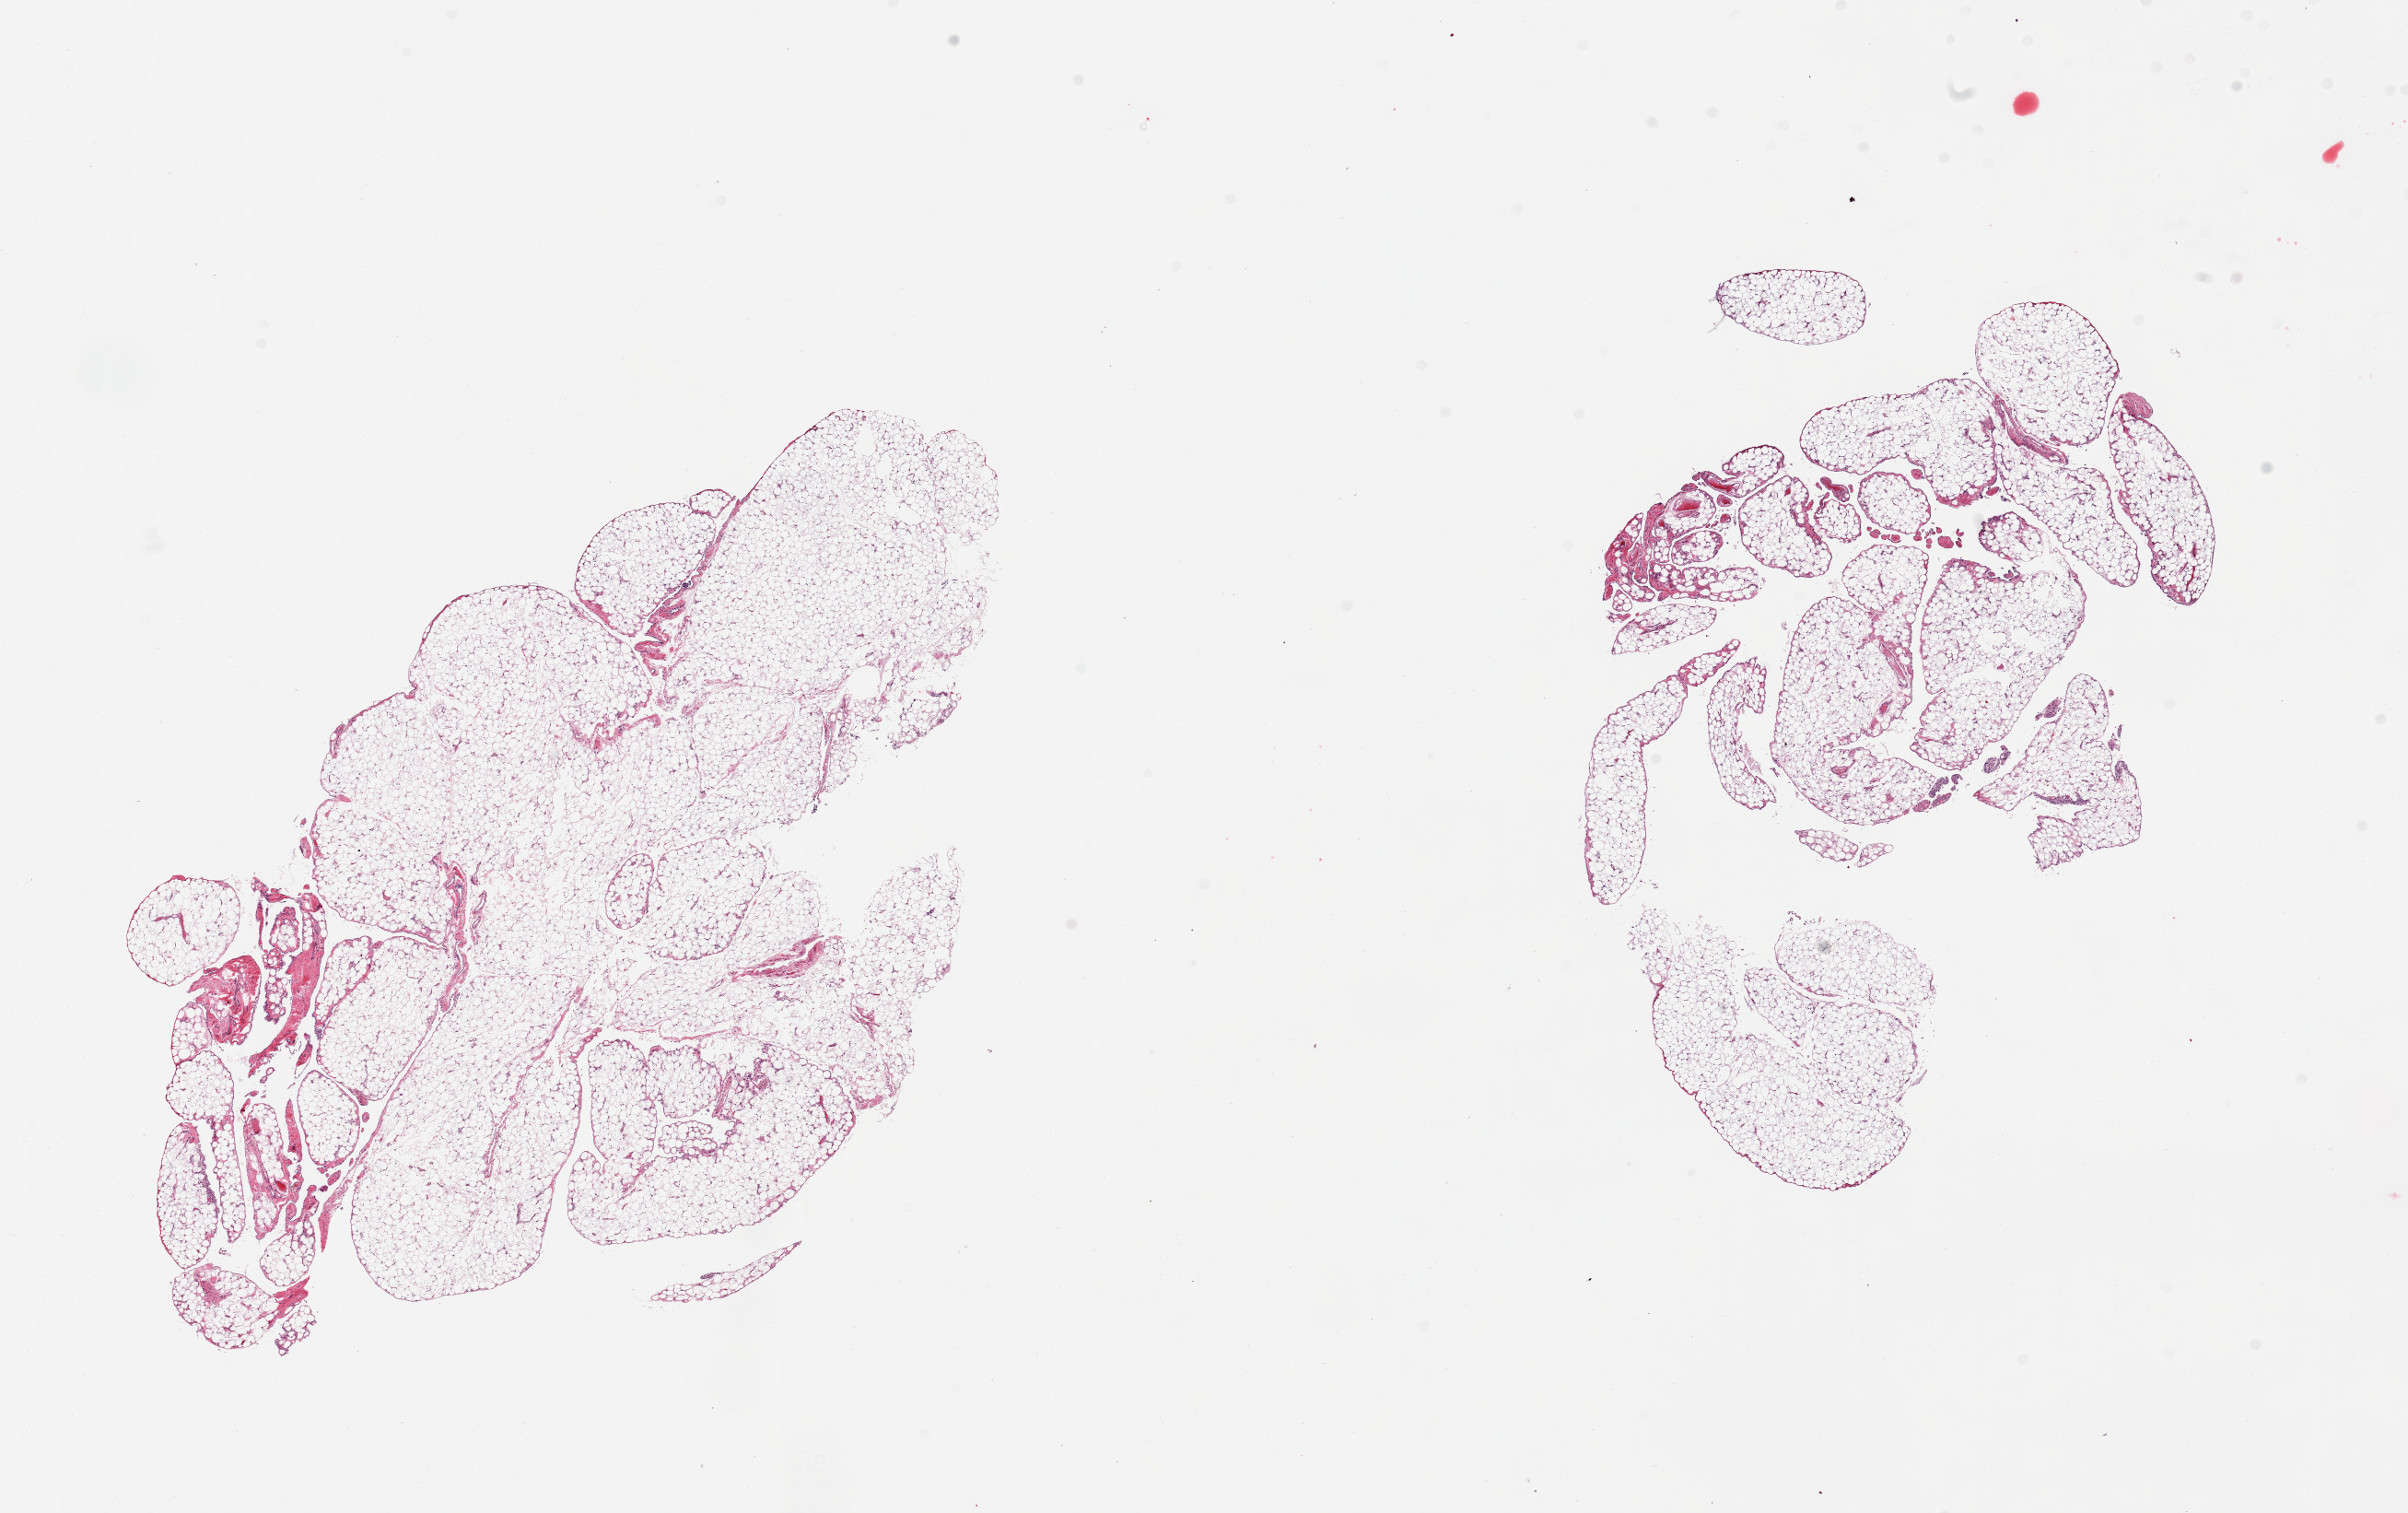
Whole-slide image, hematoxylin and eosin (H&E) stain, shown as a low-resolution overview of the whole scanned area (about 20.7 x 13.0 mm). PAXgene-fixed paraffin-embedded (PFPE) section. Sampled site (target tissue): omentum. Tissue donor sample. Donor sex: female.
• pathologist's review note for this sample: 2 pieces ~10% fascia/vascular elements